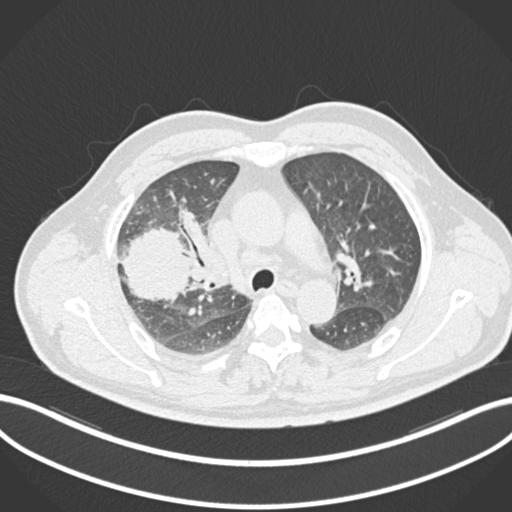
Chest CT, one axial slice; slice 656 of 852 in the series (ordered by position); reconstruction kernel B30f; 120 kVp; lung window (W 1500 / L -600 HU); 512 × 512 image matrix, field of view 400 × 400 mm. Patient: male, 55 years. From the clinical record (not read from this slice): clinical TNM (as recorded): T3 N2 M1.
Outlined on this slice (rectangle marked by the reading radiologist):
- lung tumour (recorded histology: adenocarcinoma): bounding box <116,228,195,303> (left, top, right, bottom; pixels)